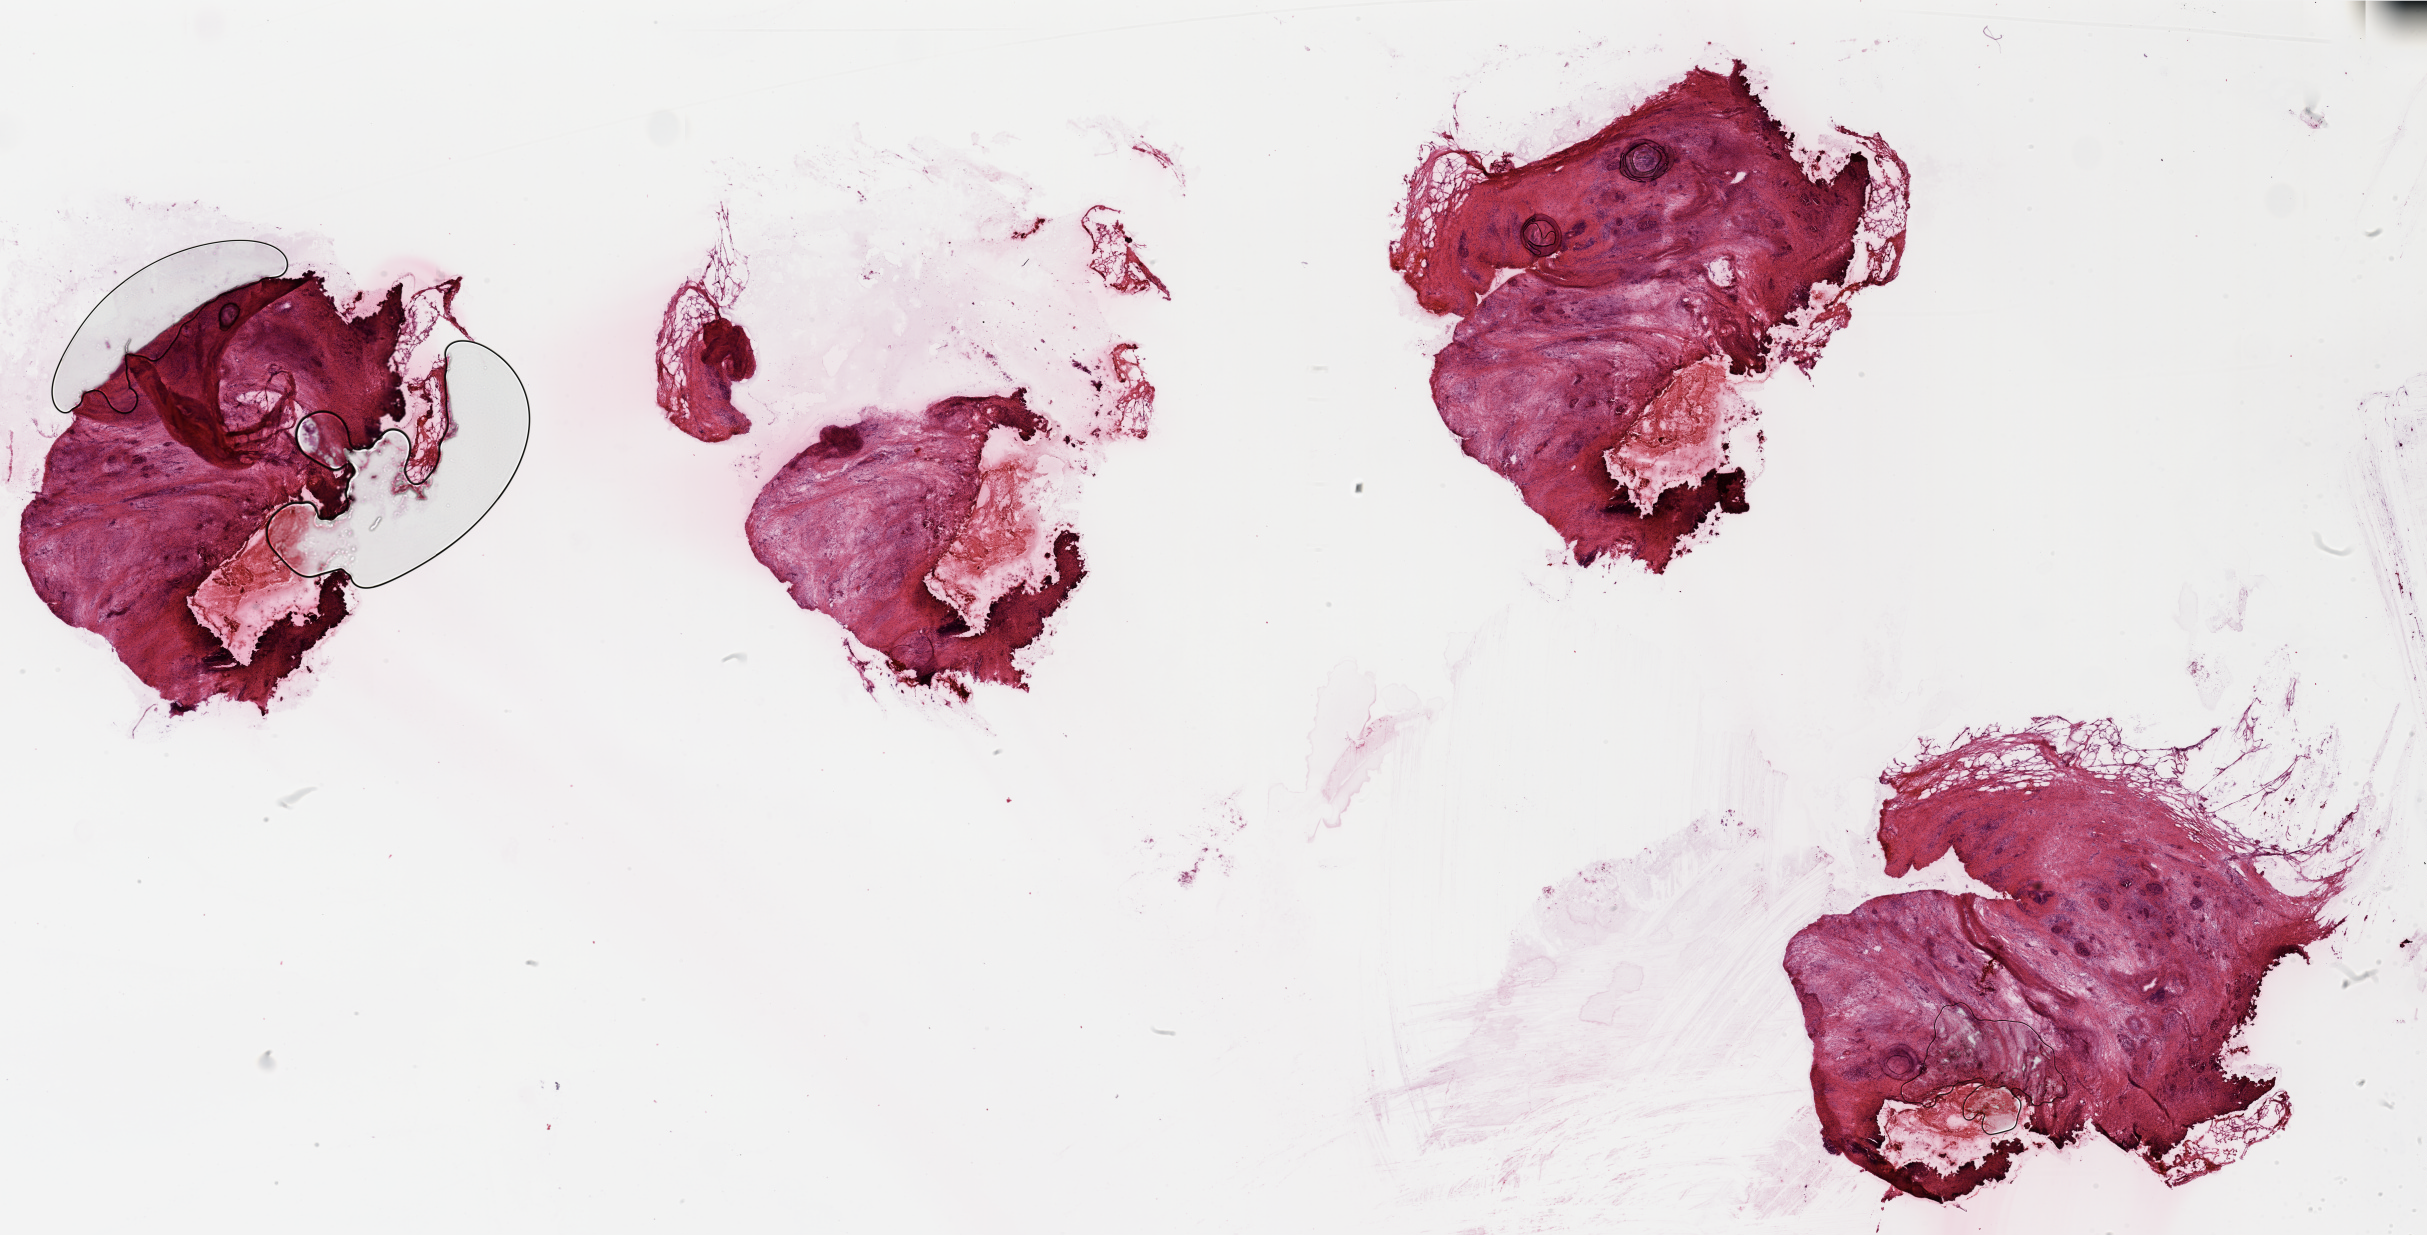
Digitized H&E-stained tissue section (whole slide) — a low-resolution overview of the entire scanned area, about 38.4 x 19.5 mm. Pancreas, normal (non-tumour) tissue. 65-year-old male patient.
This section: normal (non-tumour) tissue from the same patient. Patient diagnosis: Infiltrating duct carcinoma, NOS.